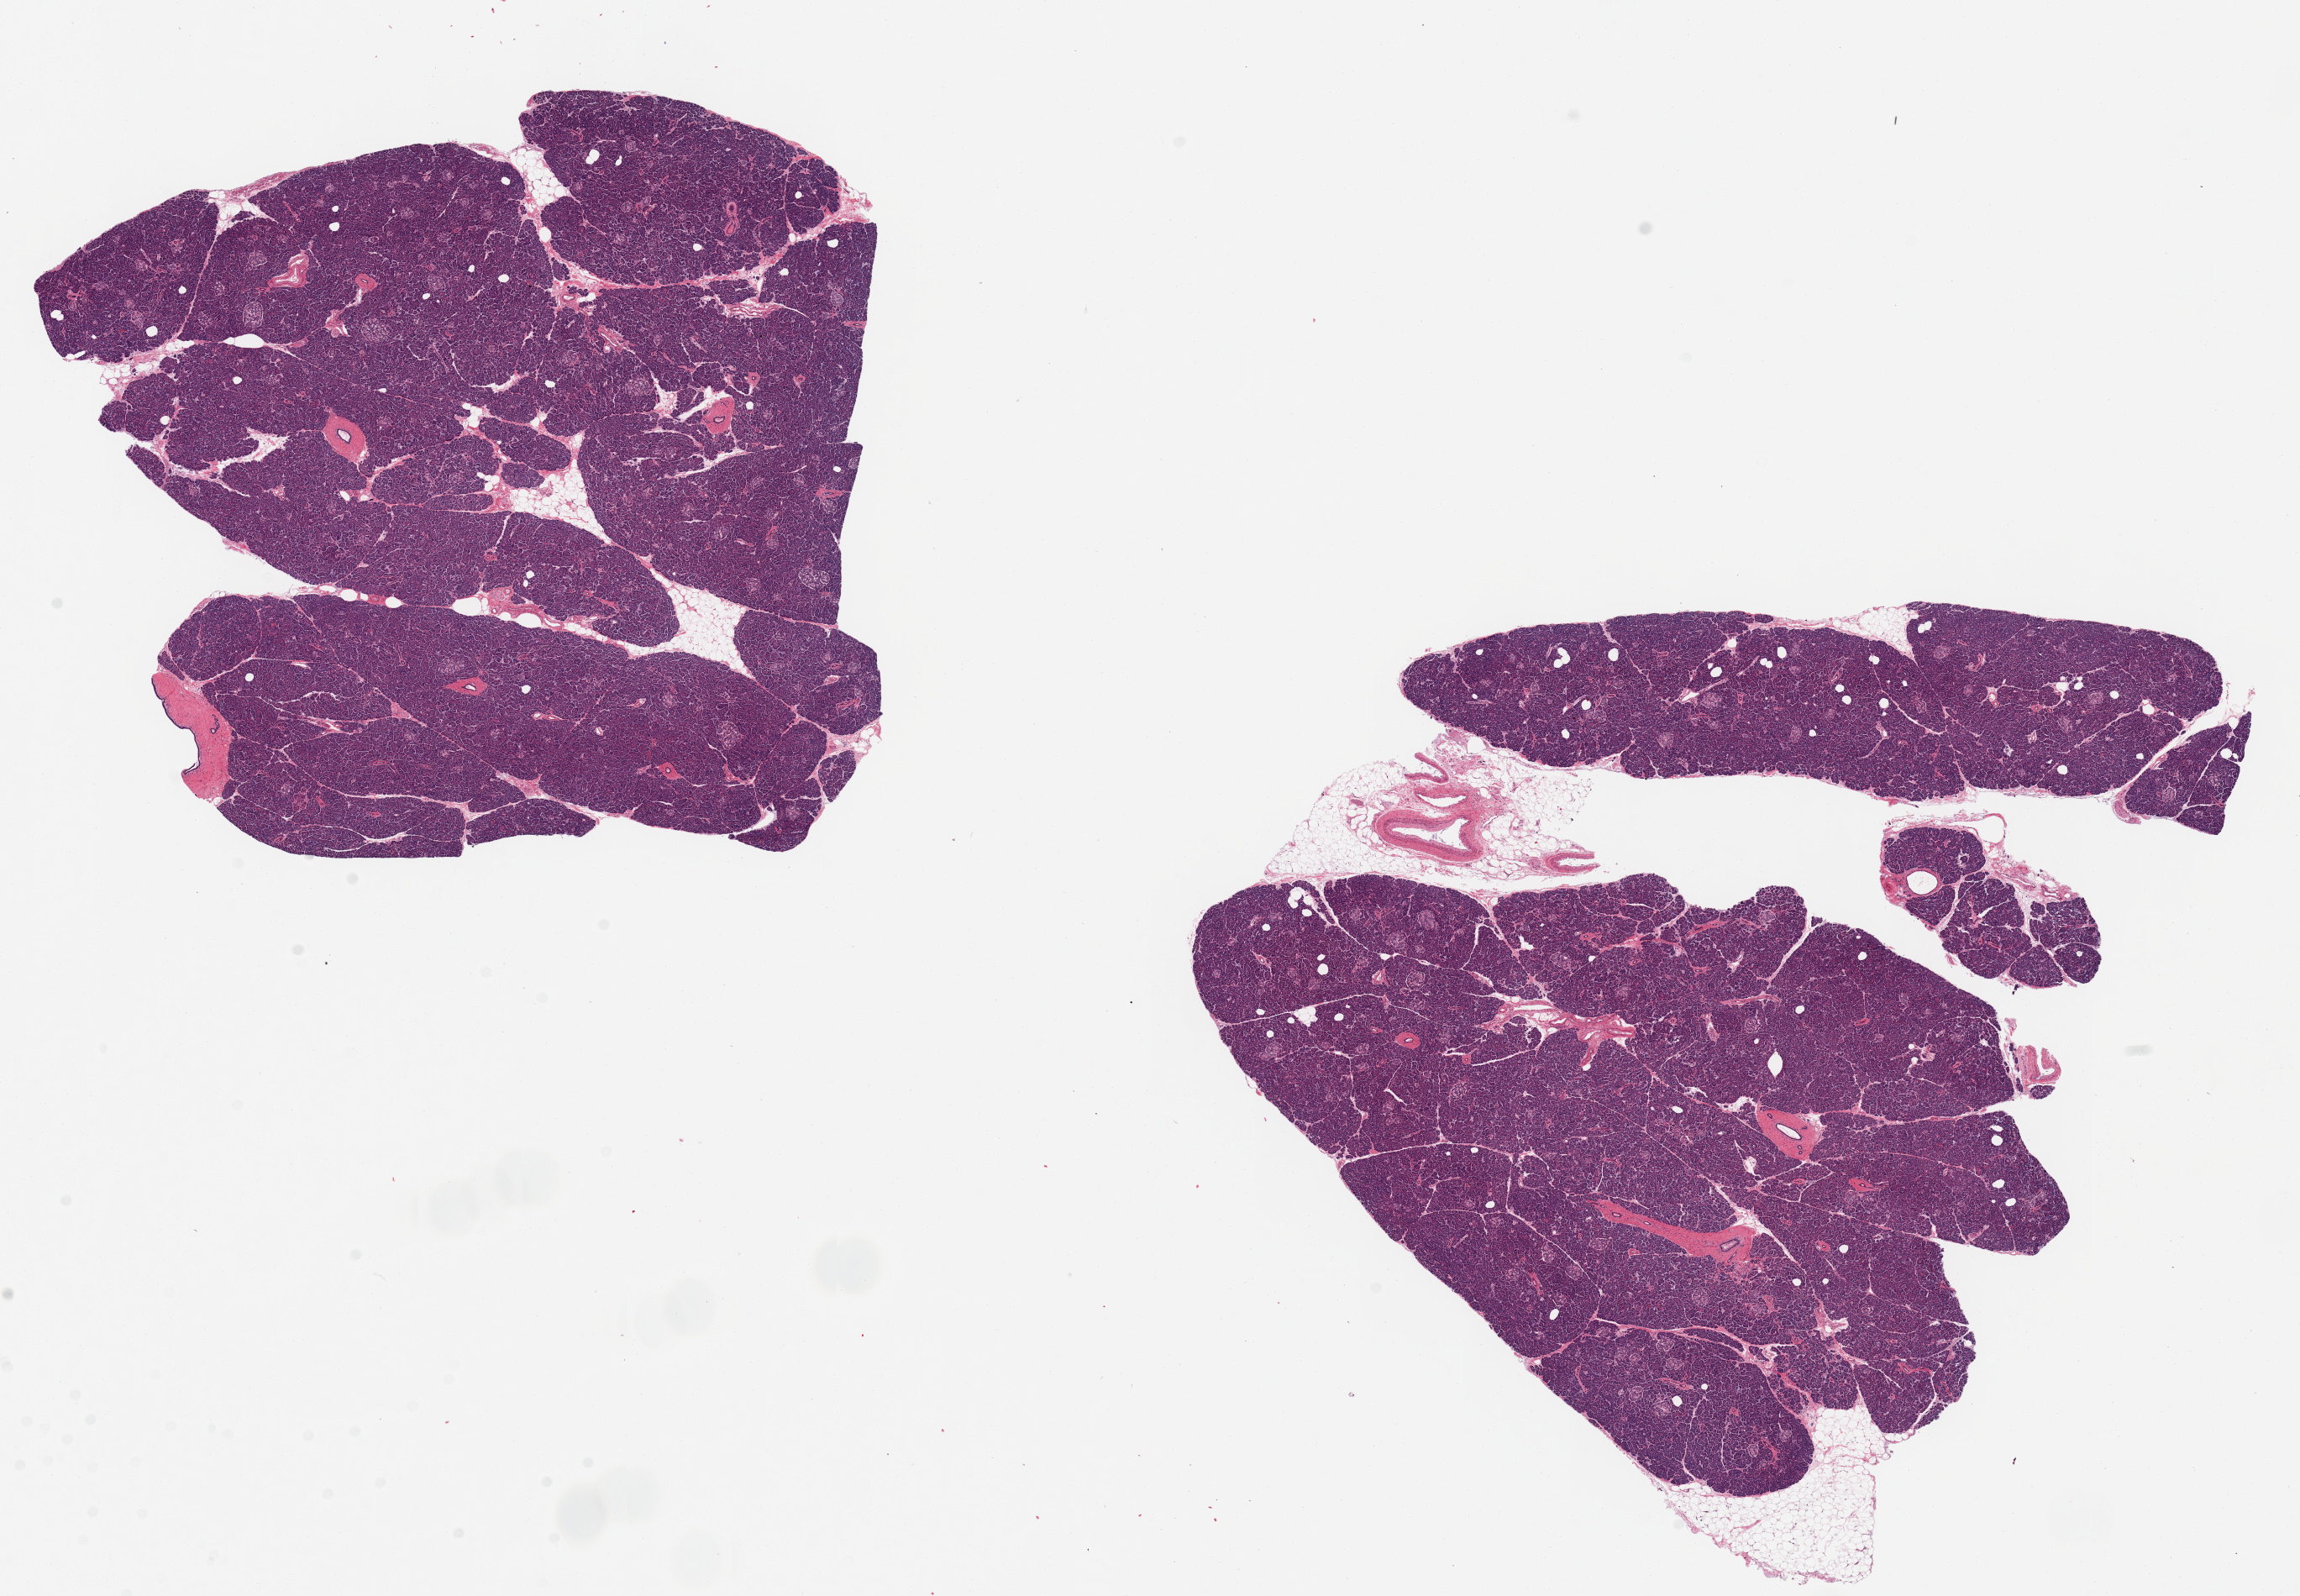
H&E whole-slide image — whole scanned area (about 21.7 x 15.0 mm, slide scanned at 20x) shown as a low-resolution overview, PAXgene-fixed paraffin-embedded (PFPE) section, section of pancreas (target tissue), donor tissue sample. Donor sex: female.
Pathologist's review note for this sample: 2 pieces, 10x9 & 8x7mm; well presrved, minimal fat, Islets well visualized.